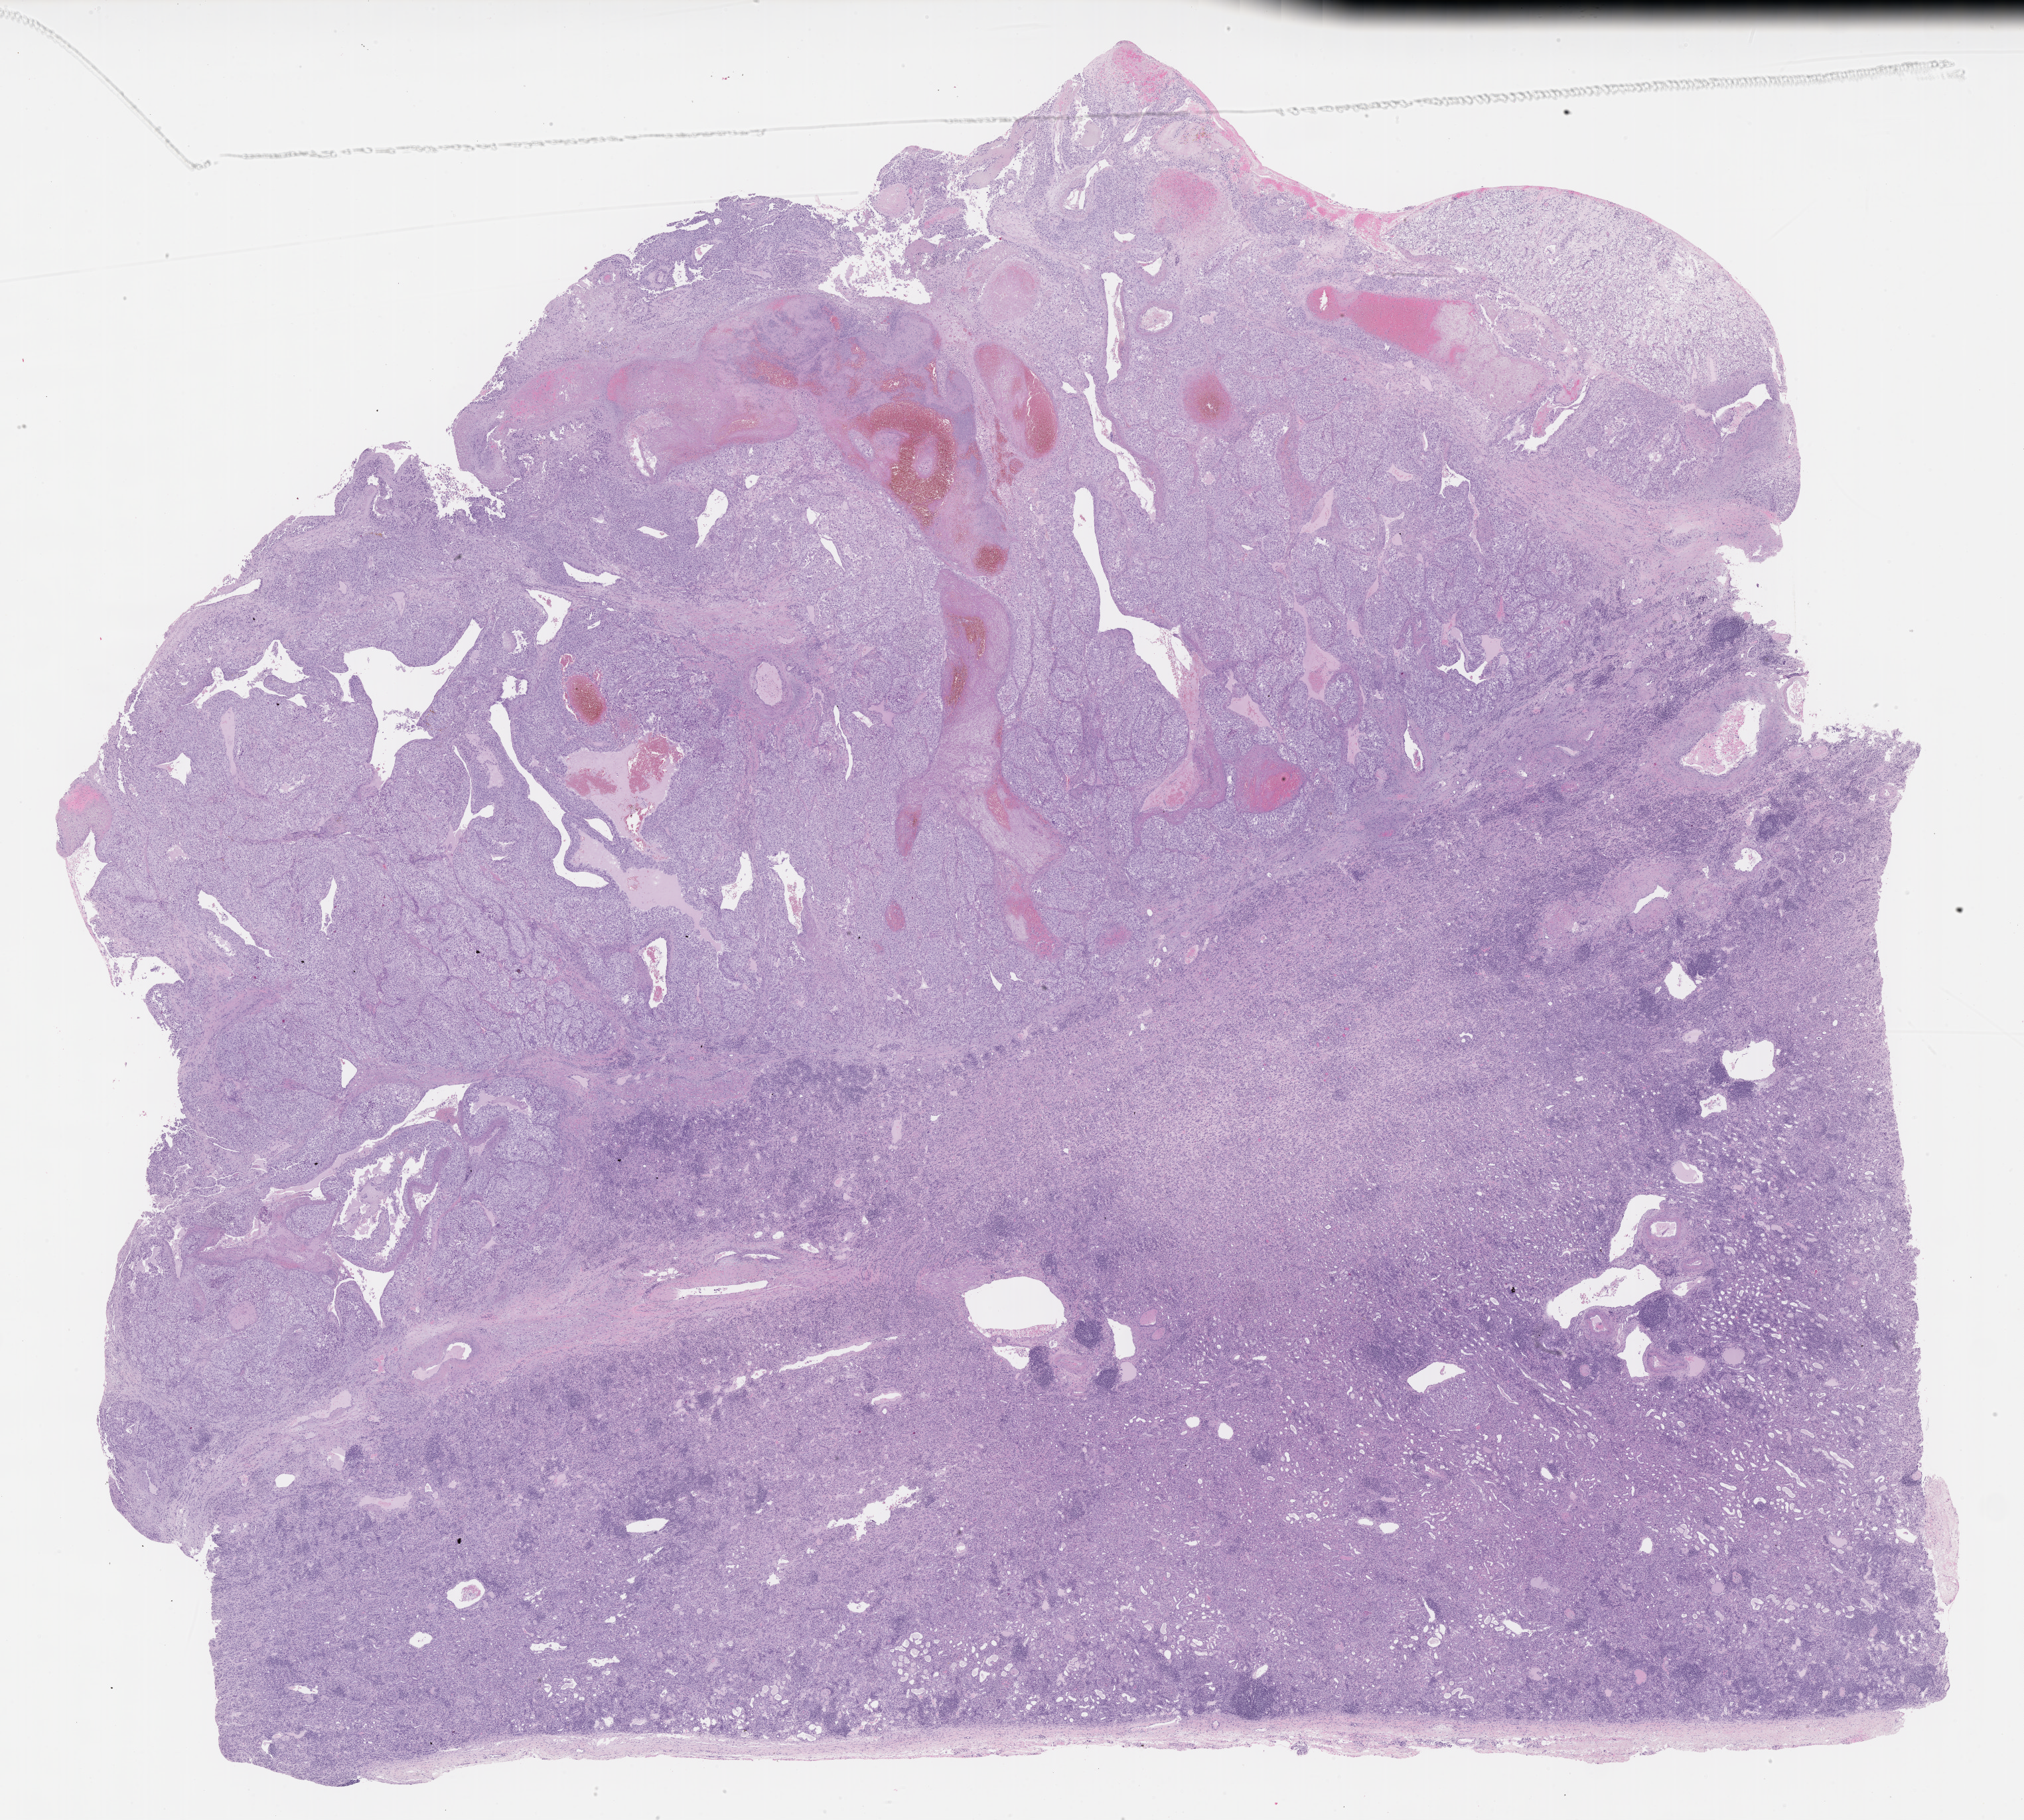
H&E-stained whole-slide image — a low-resolution overview of the entire scanned area, about 24.7 x 22.2 mm (slide scanned at 40x), FFPE section, sample: primary tumour, kidney. Female, age 54 years at initial diagnosis. Histologic grade: G4 (undifferentiated).
AJCC pathologic stage: IV. Pathologic diagnosis: Clear cell adenocarcinoma, NOS.